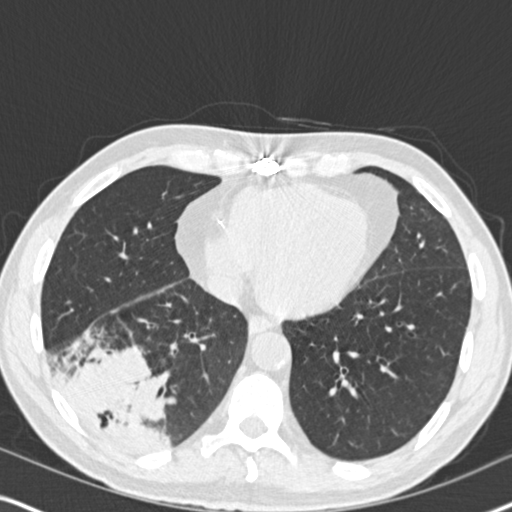
Low-dose screening chest CT, one axial slice; slice 70 of 182 in the series (ordered by position); reconstruction kernel B30f; 120 kVp; lung window (W 1500 / L -600 HU); 512 × 512 image matrix, field of view 330 × 330 mm.
Outlined on this slice (outlined manually by an expert reader):
- lesion 1 (tumor, lower lobe of right lung): bounding box (x1, y1, x2, y2) in pixels: (68, 350, 167, 452)